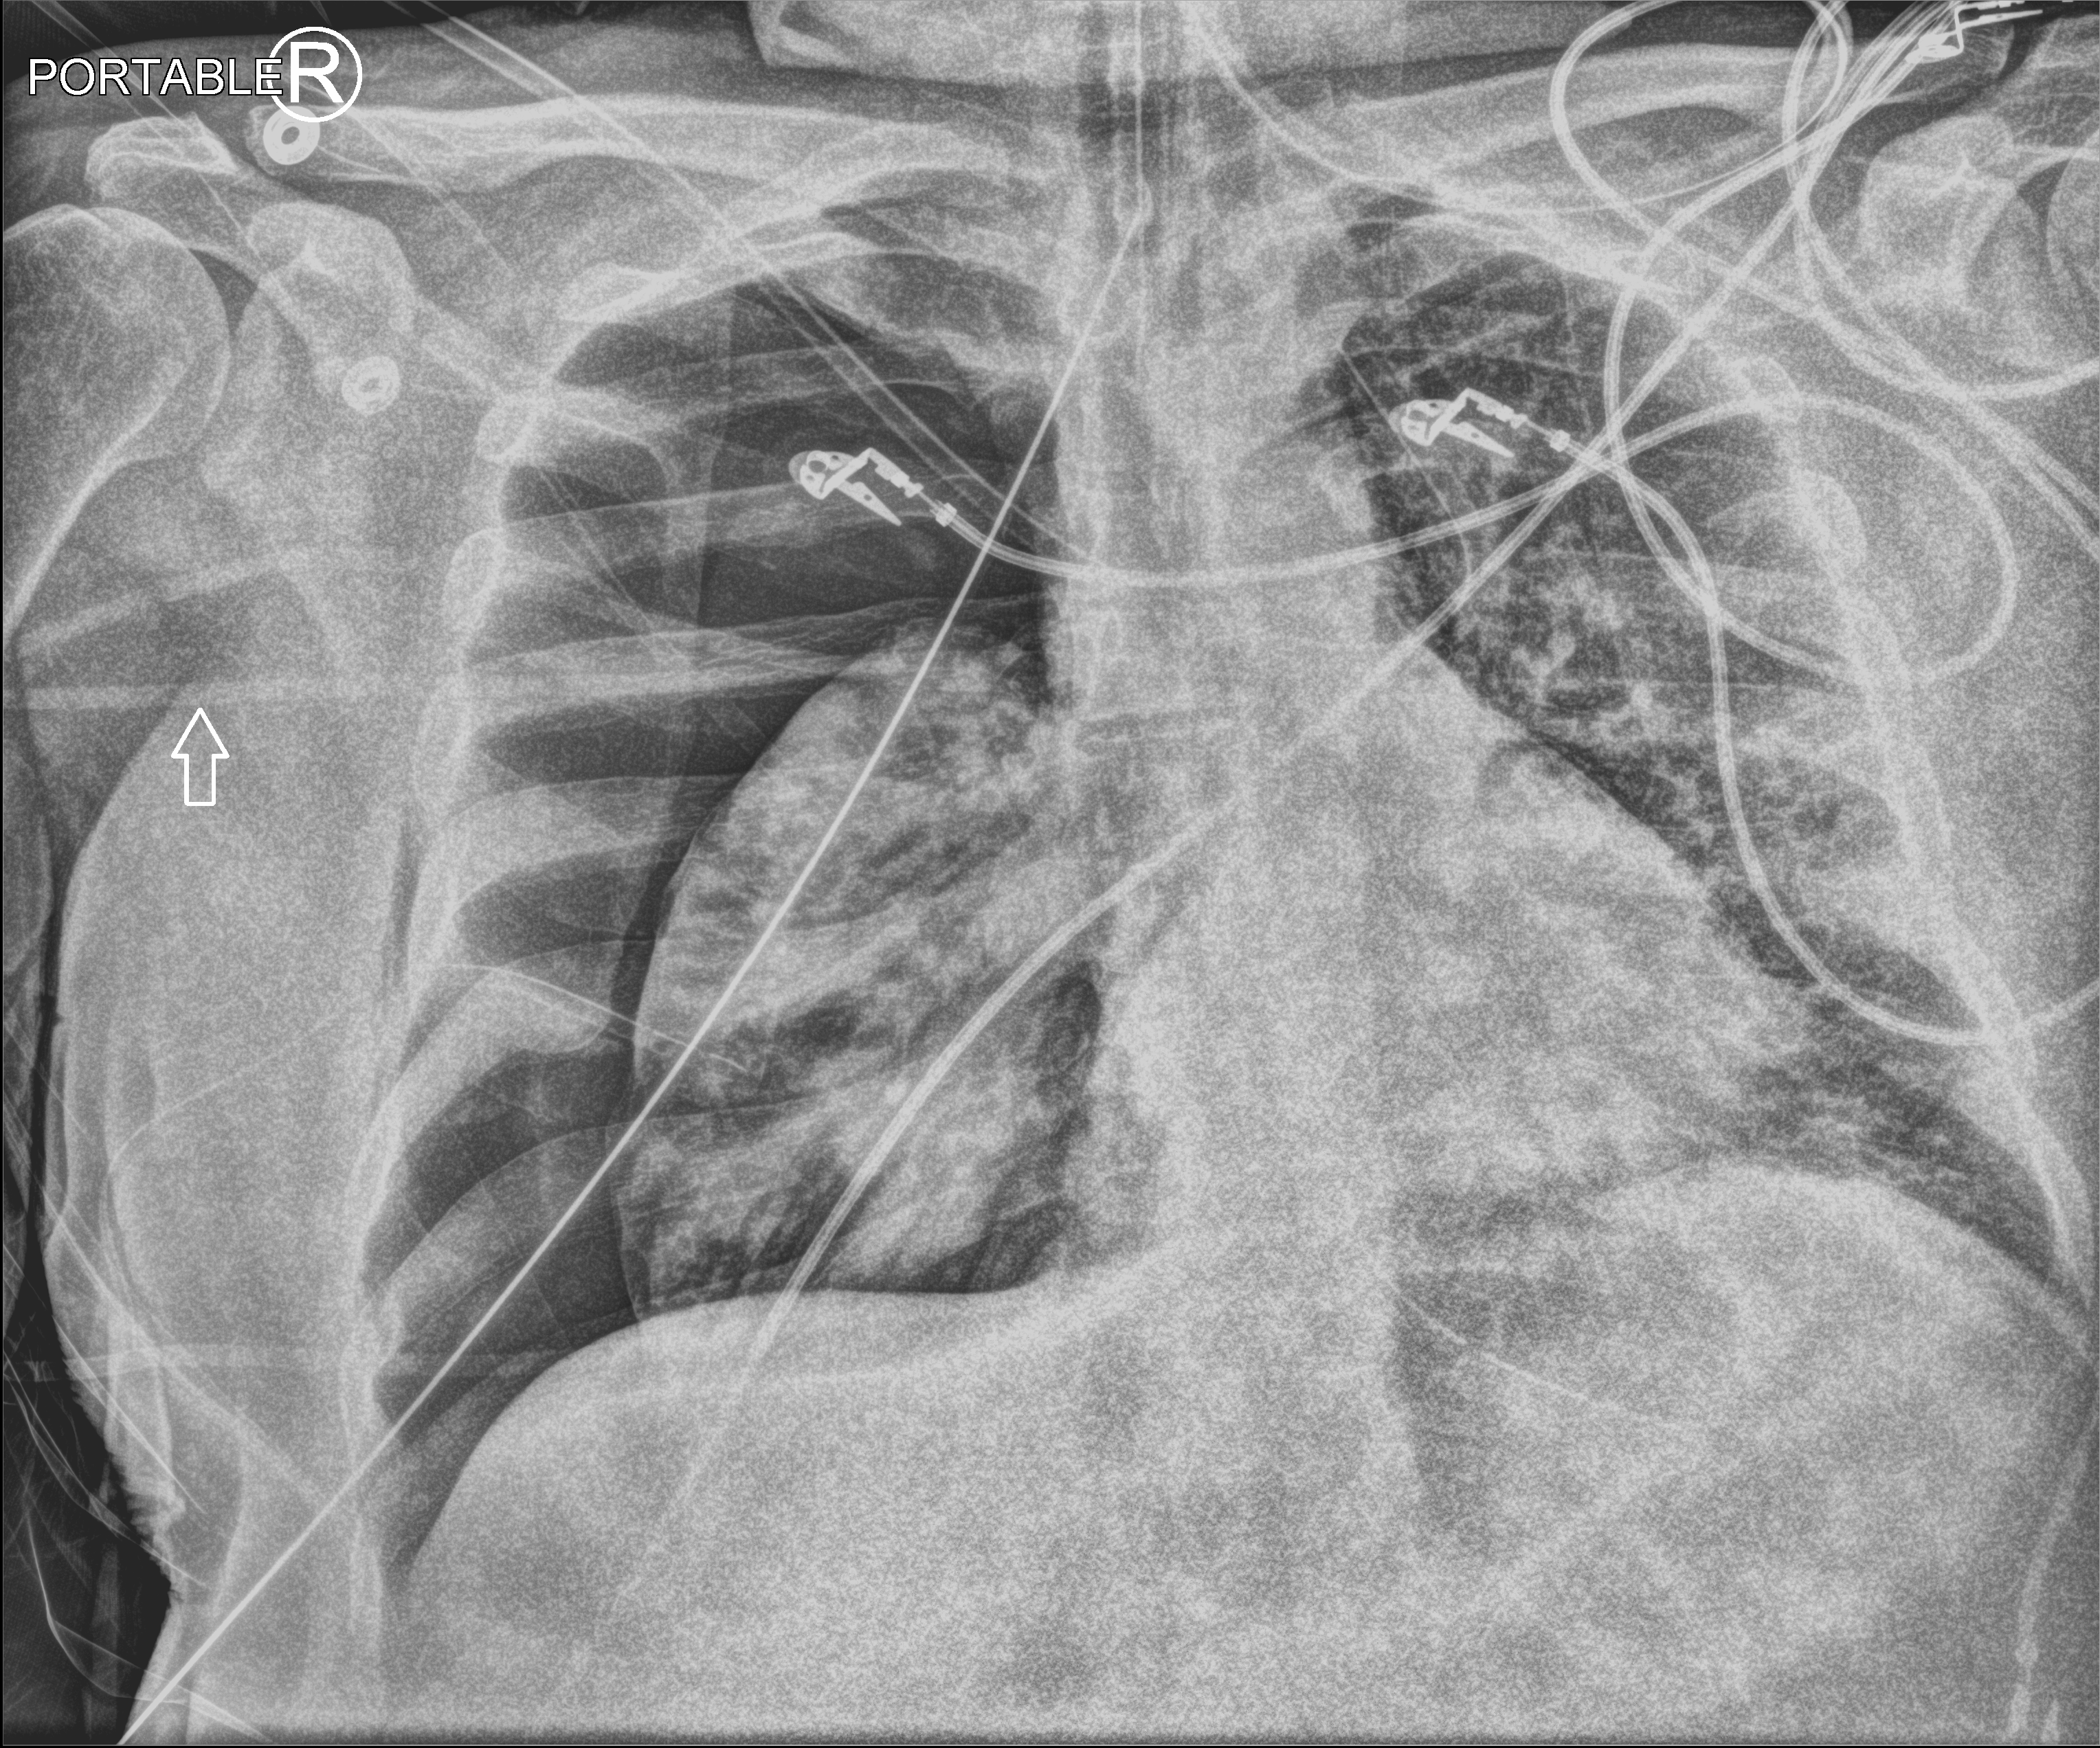
Bedside chest radiograph (computed radiography), anteroposterior (AP) projection. Patient hospitalised with COVID-19; male, aged 18–59 years.
From the hospital-stay record, not from the radiograph (when in the stay this image was taken is not recorded): other chronic lung disease (admission record): no; COPD (admission record): no; mechanically ventilated during this hospital stay: yes.